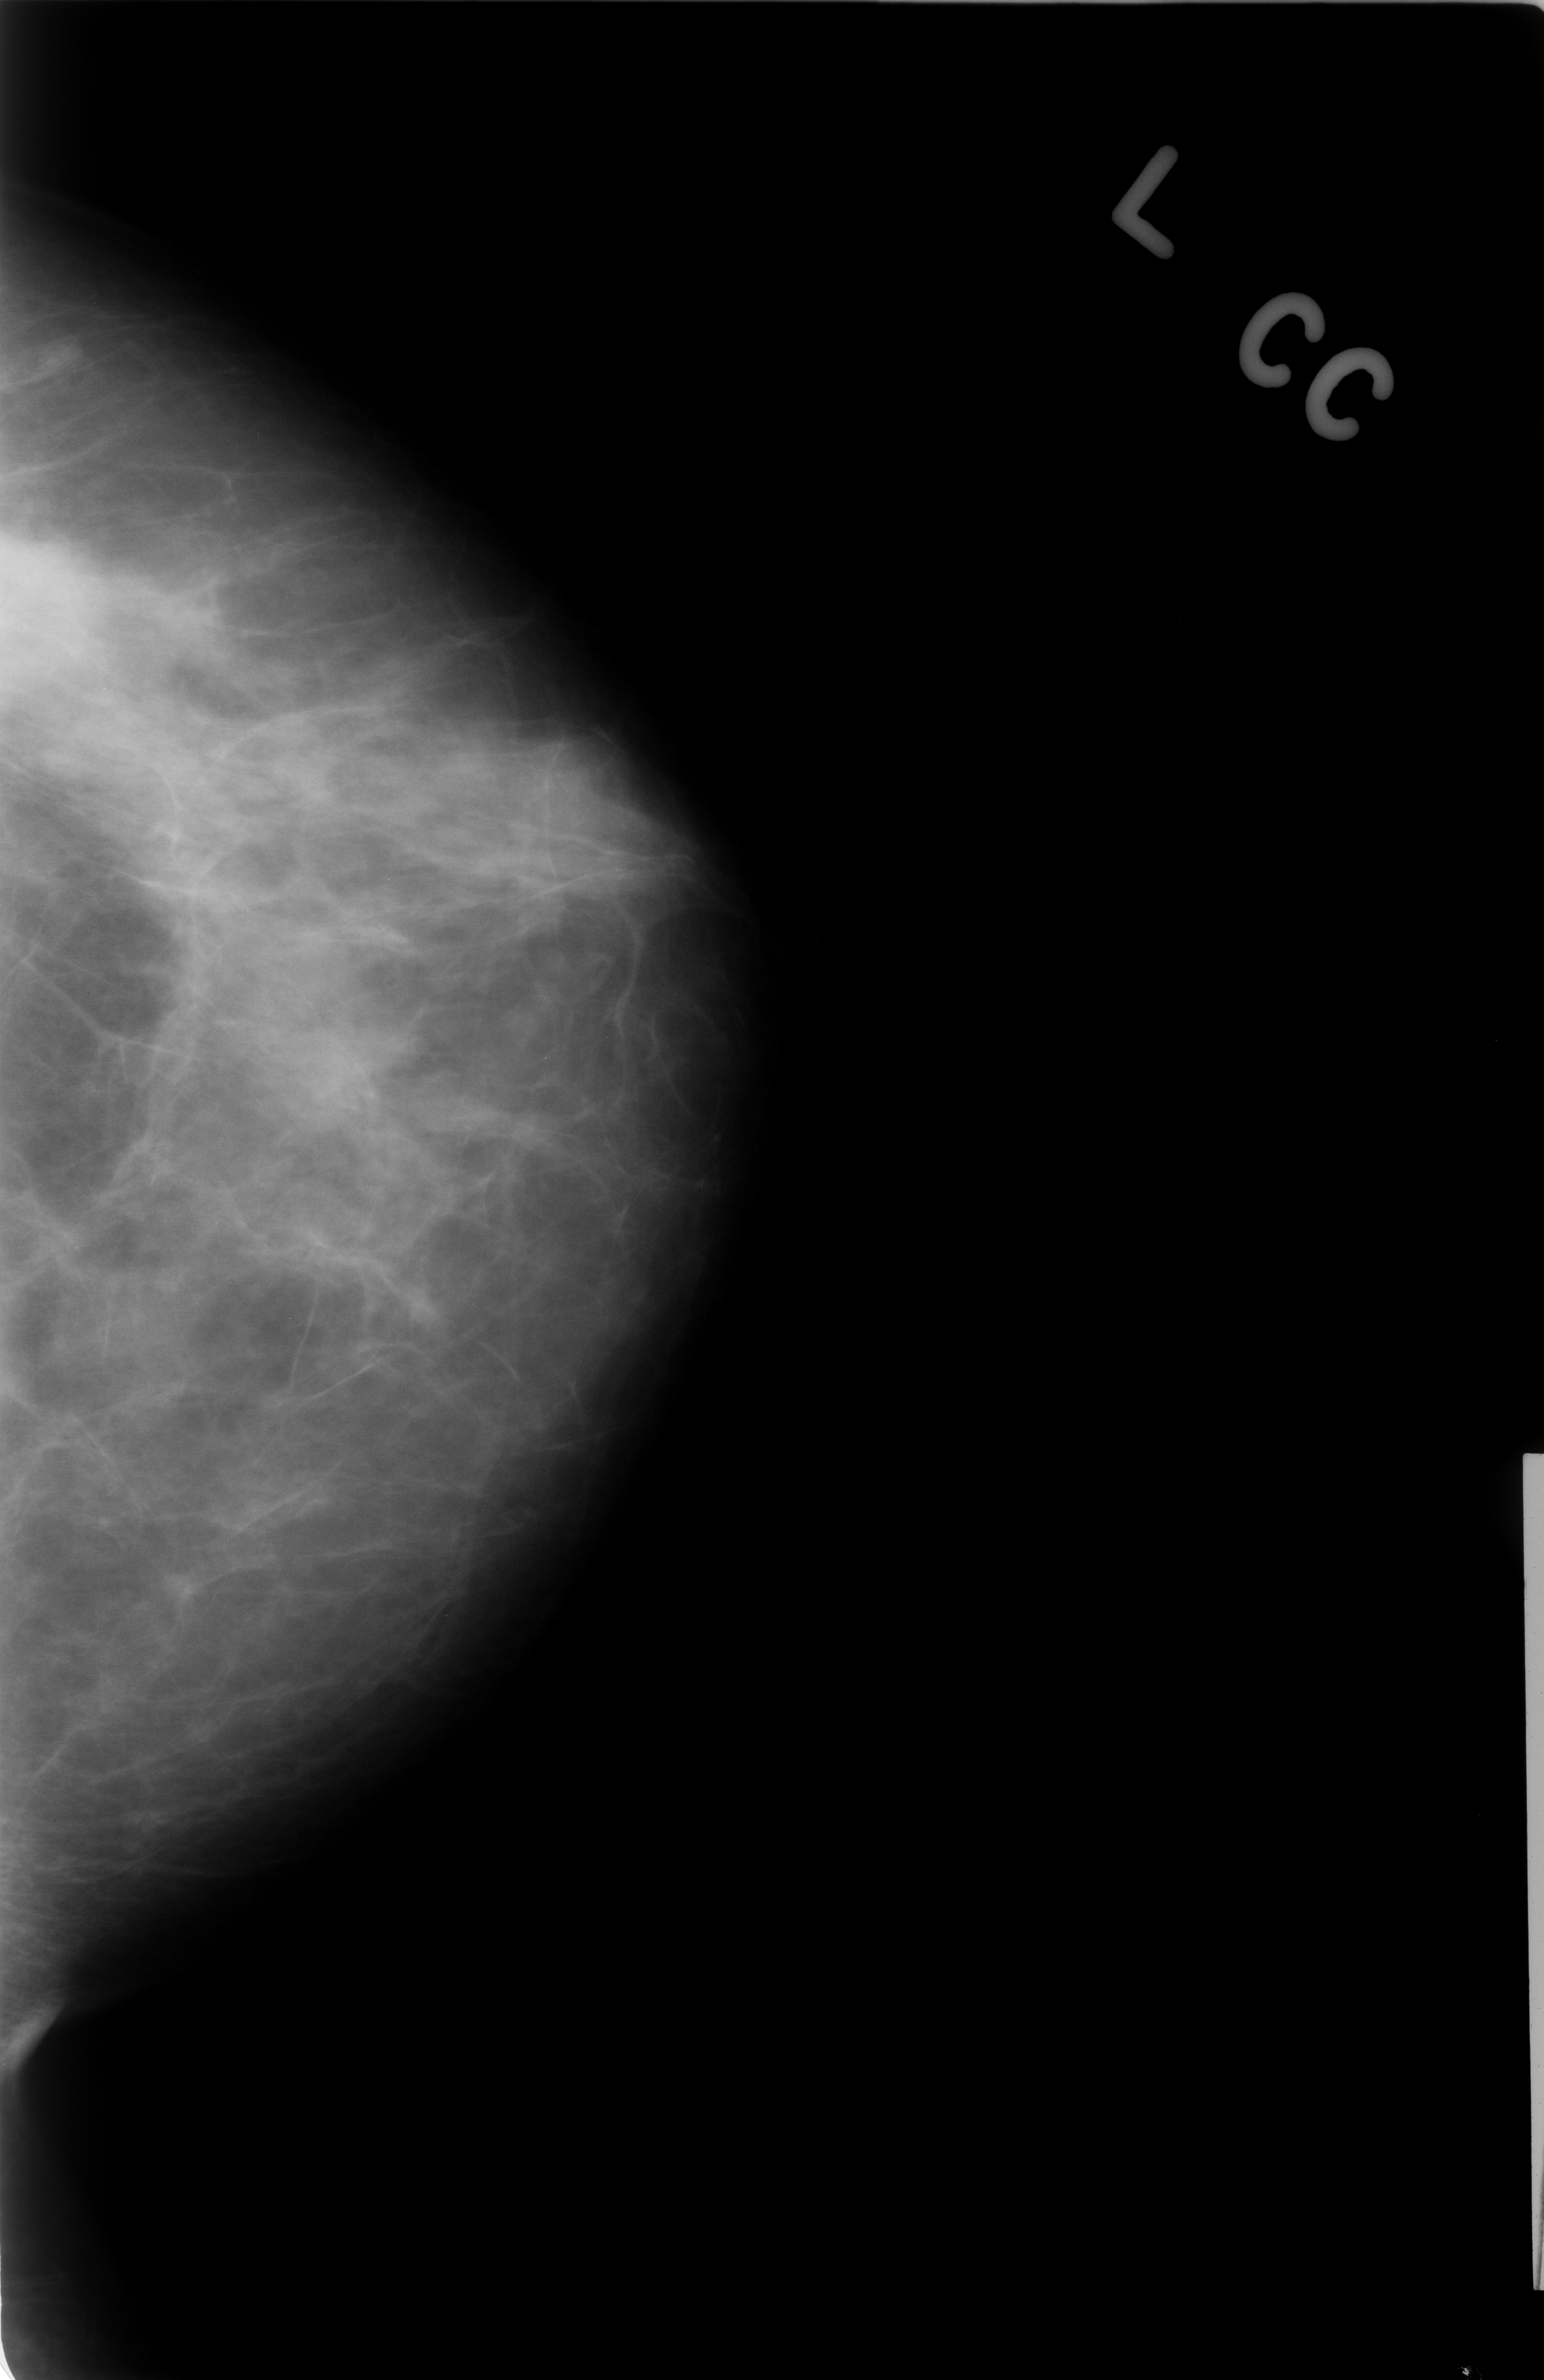
Digitized screen-film mammogram. Left breast. CC view. 1544 × 2380 image matrix.
Expert-marked regions of interest on this image (one box per marked abnormality):
- mass, shape round, margins microlobulated; BI-RADS assessment category 3; outcome (as recorded, no biopsy): benign without callback (not worked up further): box from (x=0, y=522) to (x=113, y=709) px